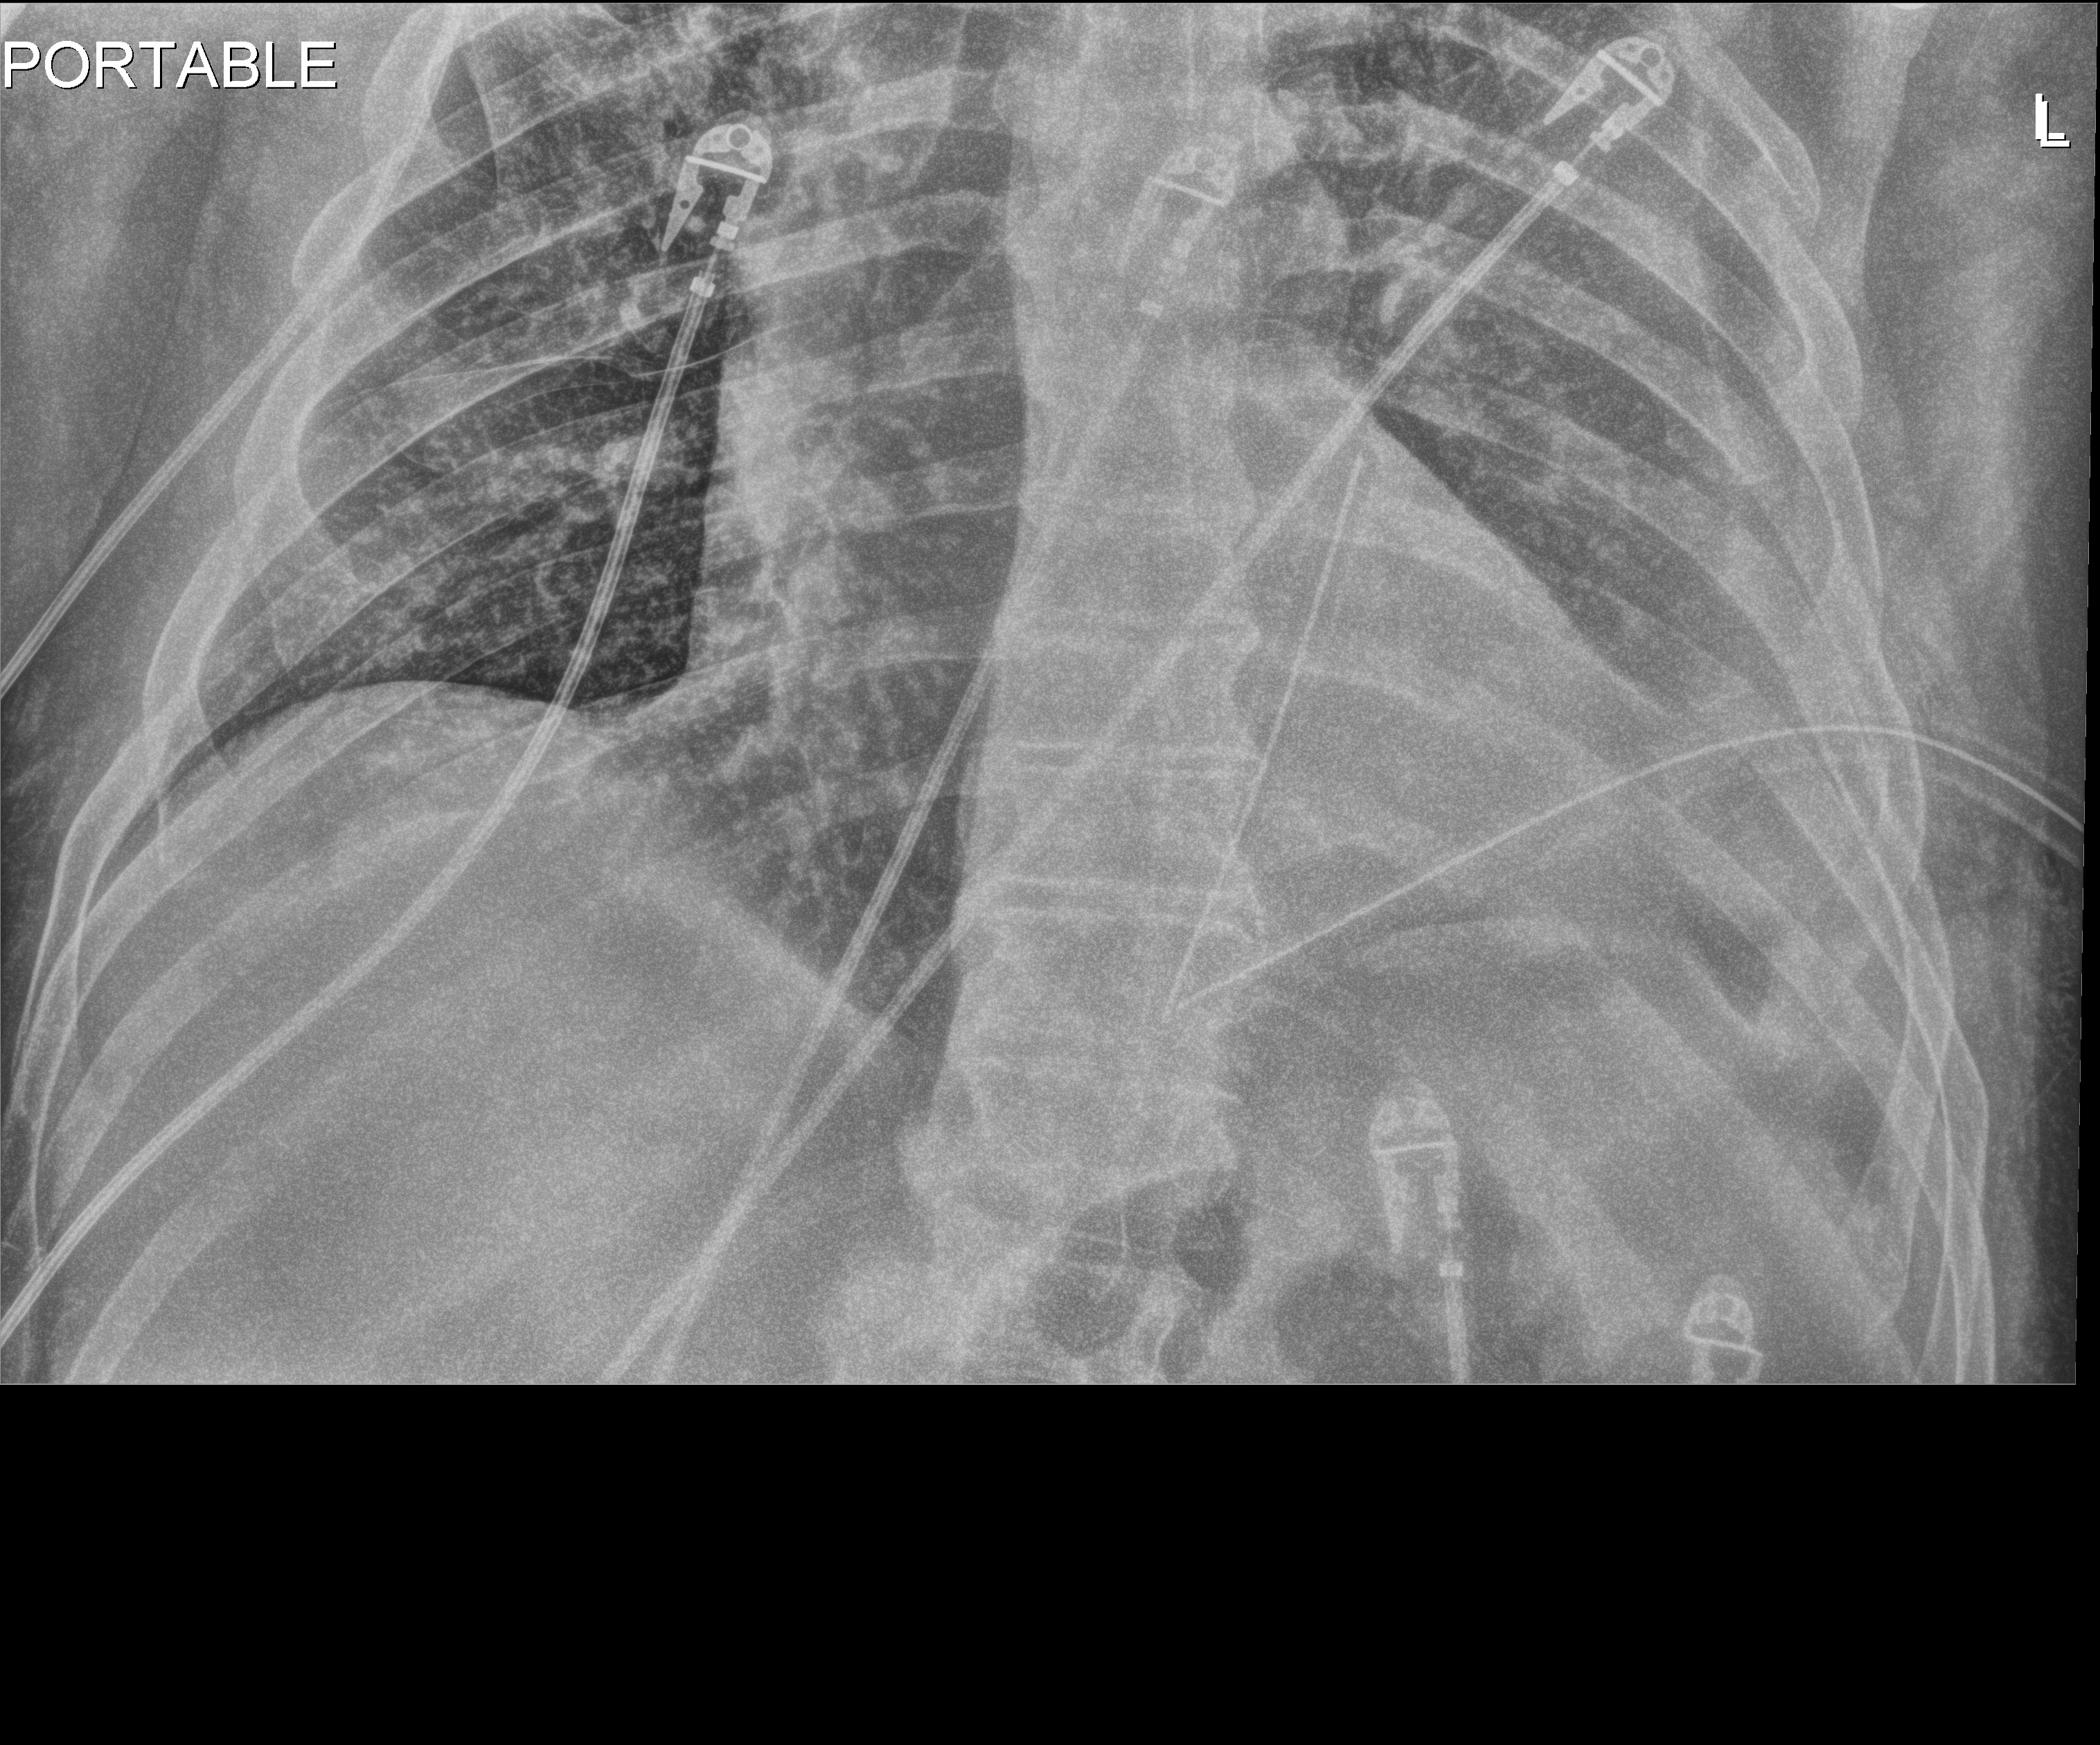
Portable chest radiograph, anteroposterior (AP) projection. Patient hospitalised with COVID-19; male, aged 18–59 years.
Hospital-stay facts (about this admission, not read from this image; timing relative to this image not recorded):
- admitted to intensive care during this hospital stay: no